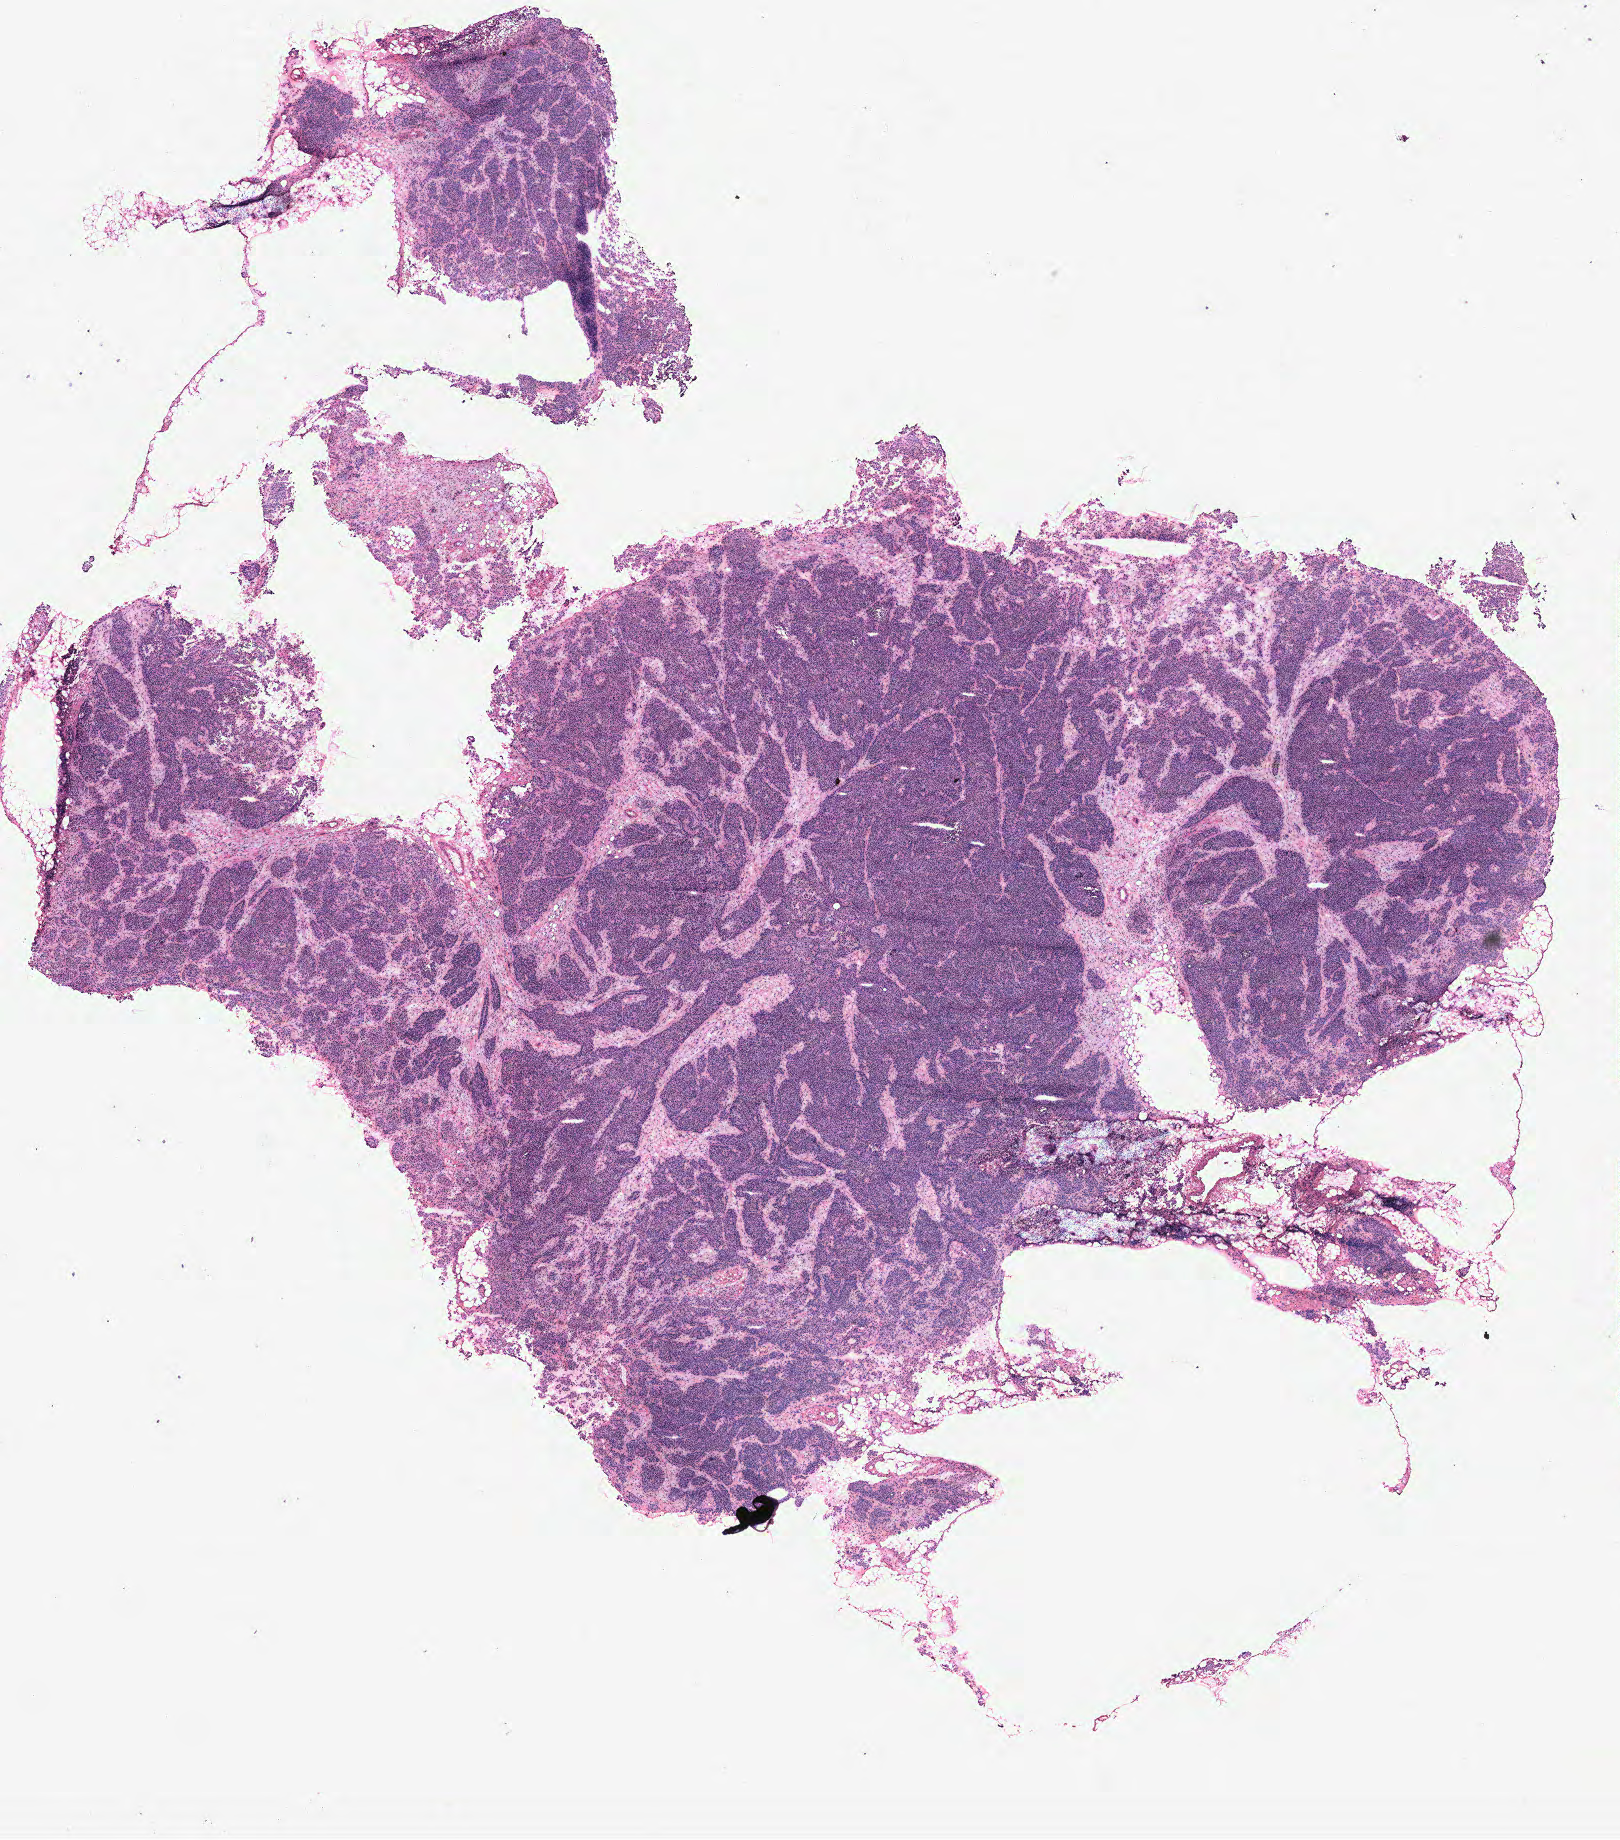
Whole-slide histology image, Hematoxylin and eosin (H&E) stained, a low-resolution overview of the entire scanned area, about 13.0 x 14.7 mm. Ovary, tissue type not recorded.
Patient diagnosis (cohort enrolment): ovarian cancer (ovary).